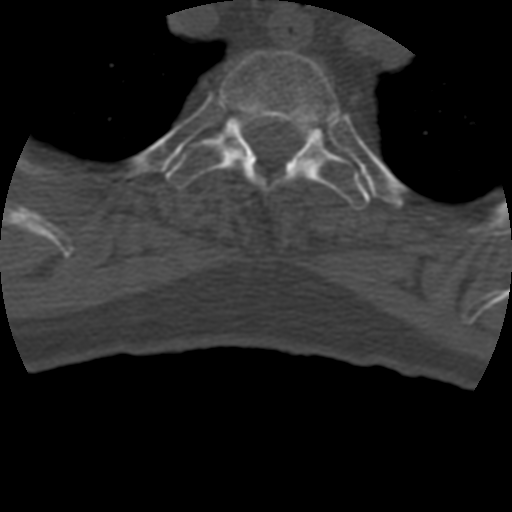
CT including the spine, one axial slice. Slice 359 of 399 in the series (ordered by position). Reconstruction kernel STANDARD. Bone window (W 1800 / L 400 HU). 1.25 mm slice thickness. 512 × 512 image matrix, field of view 160 × 160 mm. Patient age 69 years. From the clinical record (not read from this slice): primary cancer: prostate.
Annotated regions visible in this slice (semi-automatically segmented with operator editing):
- T2 vertebra: bounding box (x1, y1, x2, y2) in pixels: (218, 51, 343, 126)
- T3 vertebra: (165, 113, 371, 210)